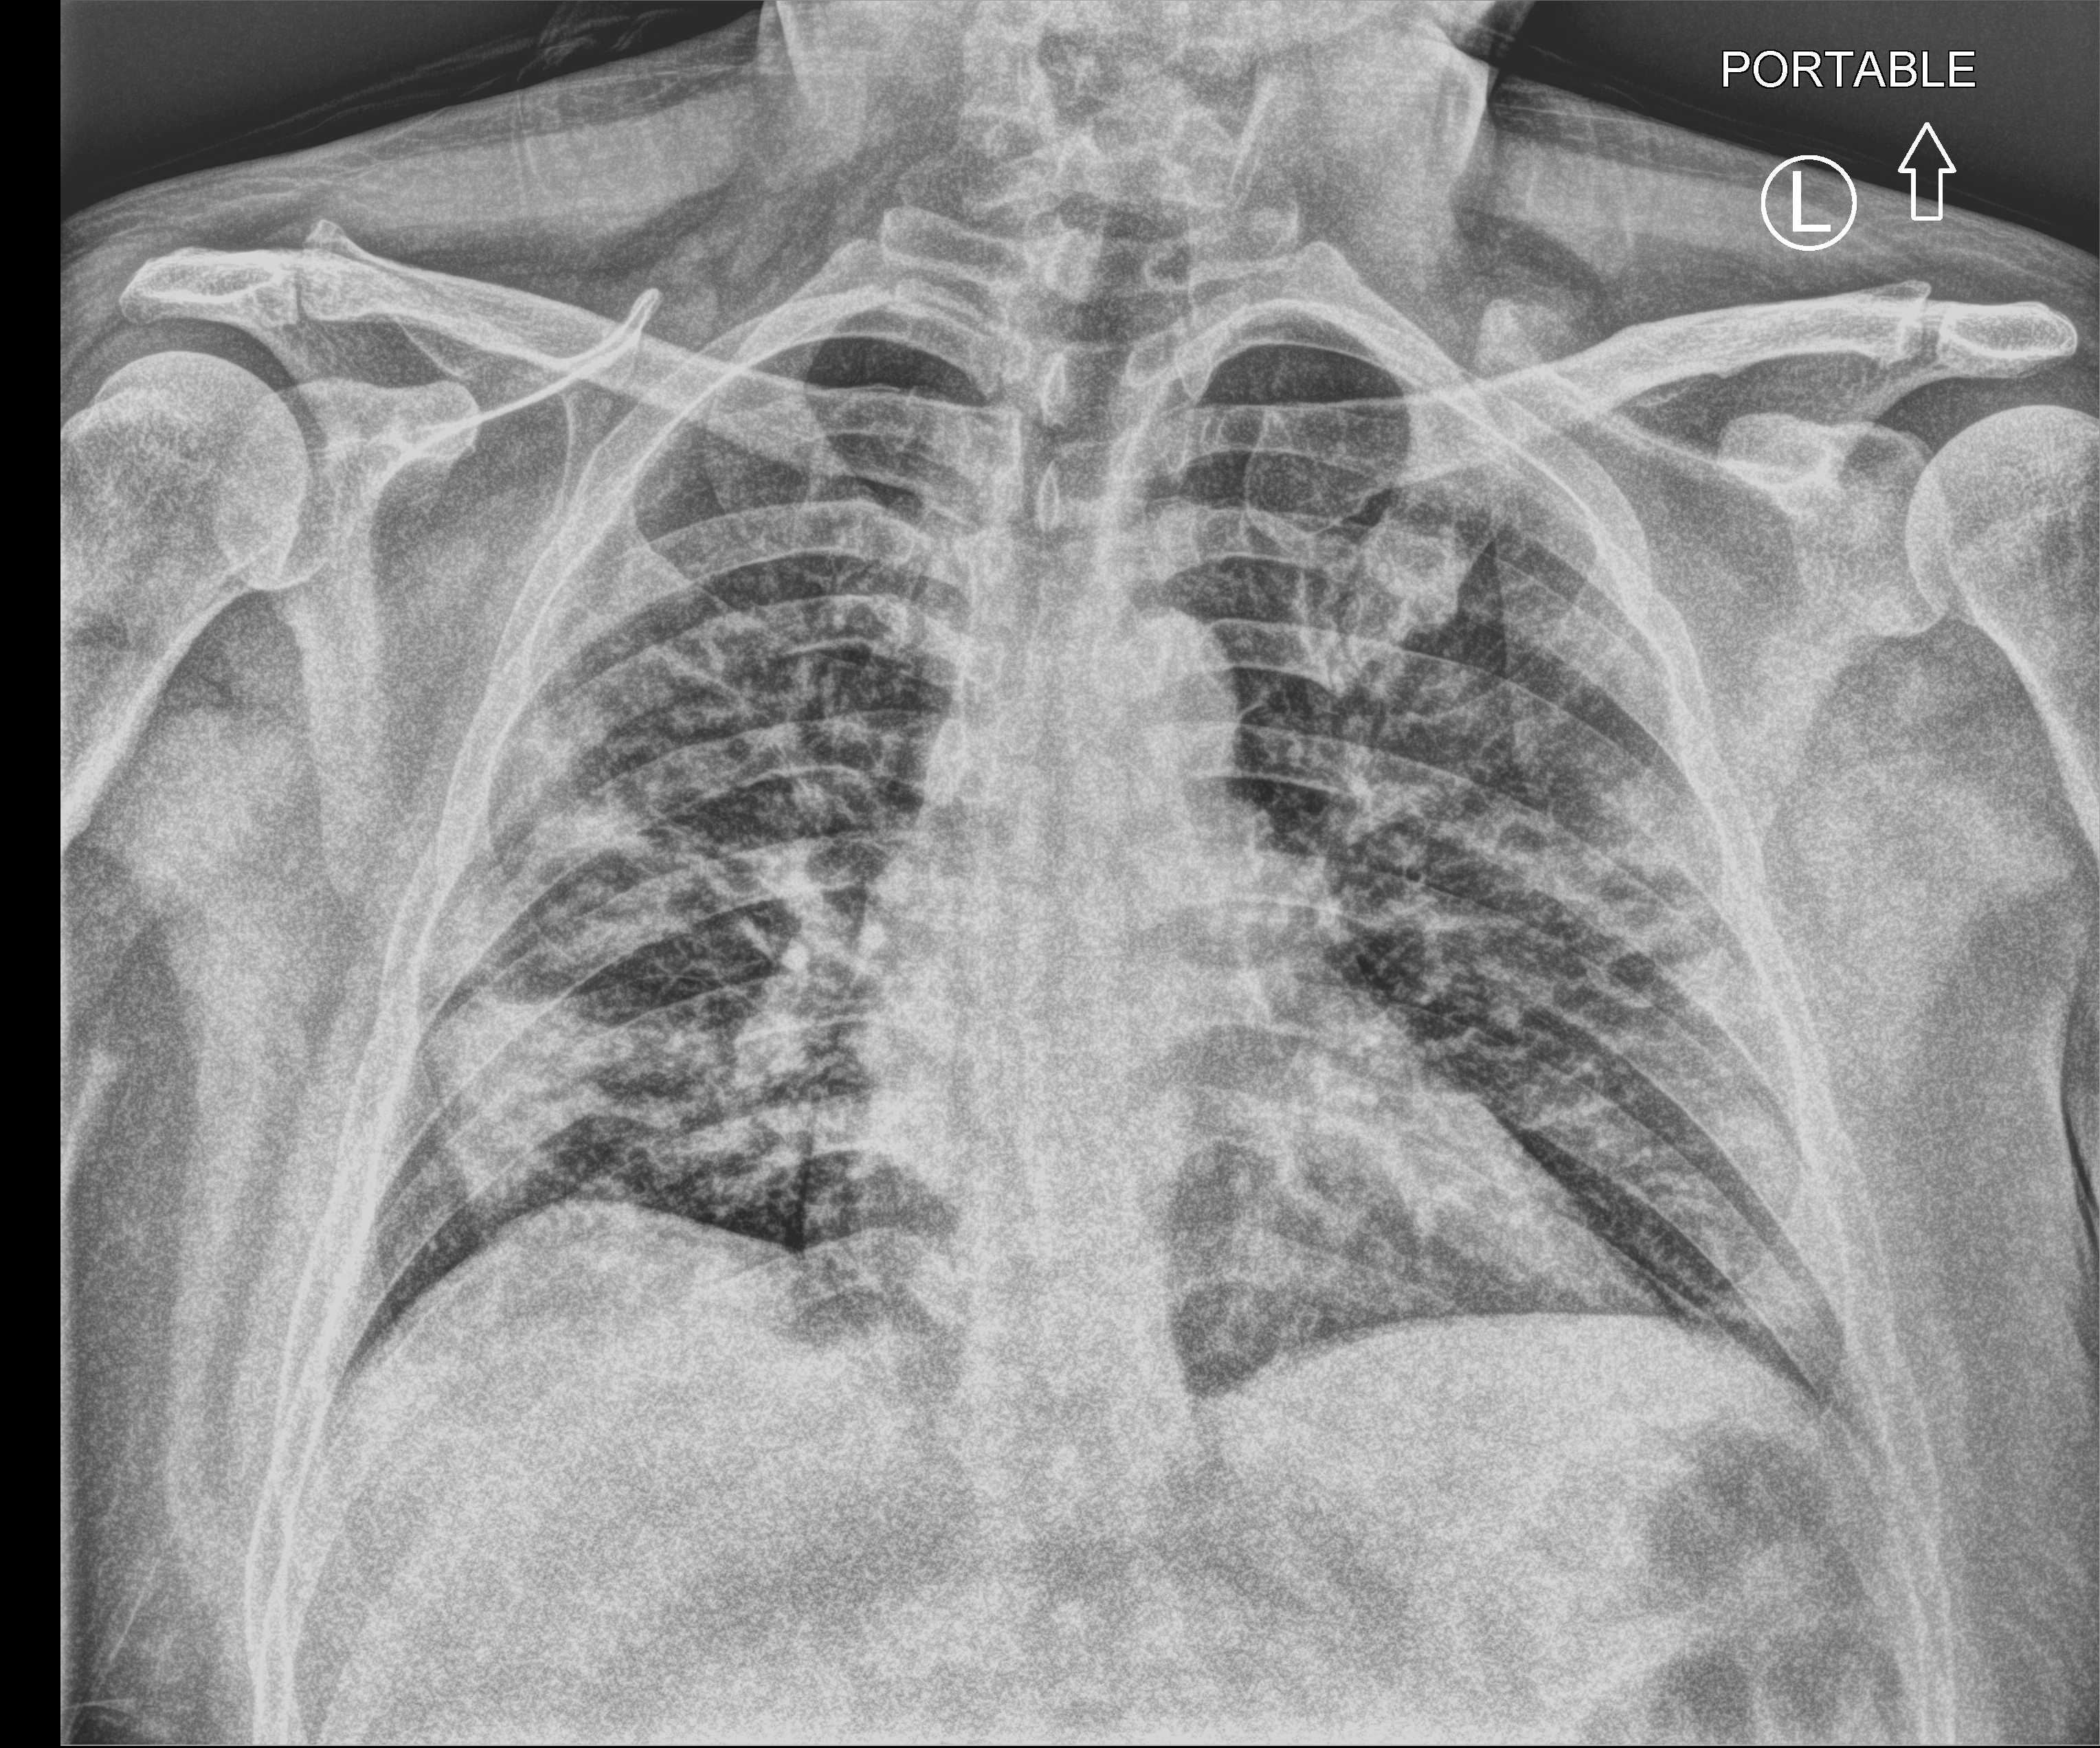
Portable chest radiograph, anteroposterior (AP) projection. Male patient hospitalised with COVID-19, age 18–59 years.
From the hospital-stay record, not from the radiograph (when in the stay this image was taken is not recorded): length of hospital stay: 1 day.